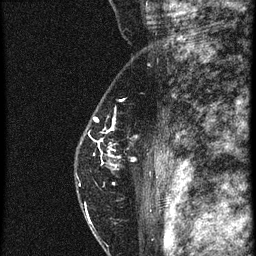
Breast MRI (dynamic contrast-enhanced), one sagittal slice. Position 42 of 60 along the scan axis. 4 images stored at this slice position (order not interpretable as contrast timing). 1.5 T. TE 4.2 ms, TR 20.4 ms. 1.5 mm slice thickness. 256 × 256 image matrix, field of view 180 × 180 mm. Patient: female, 46 years. Case-level facts recorded for this patient, not image findings: setting: breast cancer imaged before/during neoadjuvant chemotherapy; receptor status: triple-negative.
Outlined on this slice (semi-automatically segmented with operator editing):
- analysis volume of interest (the breast-tissue region the enhancement analysis was run in; not a lesion): bounding box <74,82,159,201> (left, top, right, bottom; pixels)
- tumour enhancement mask (voxels above the 90 % enhancement threshold inside the analysis volume of interest): <80,130,137,187>